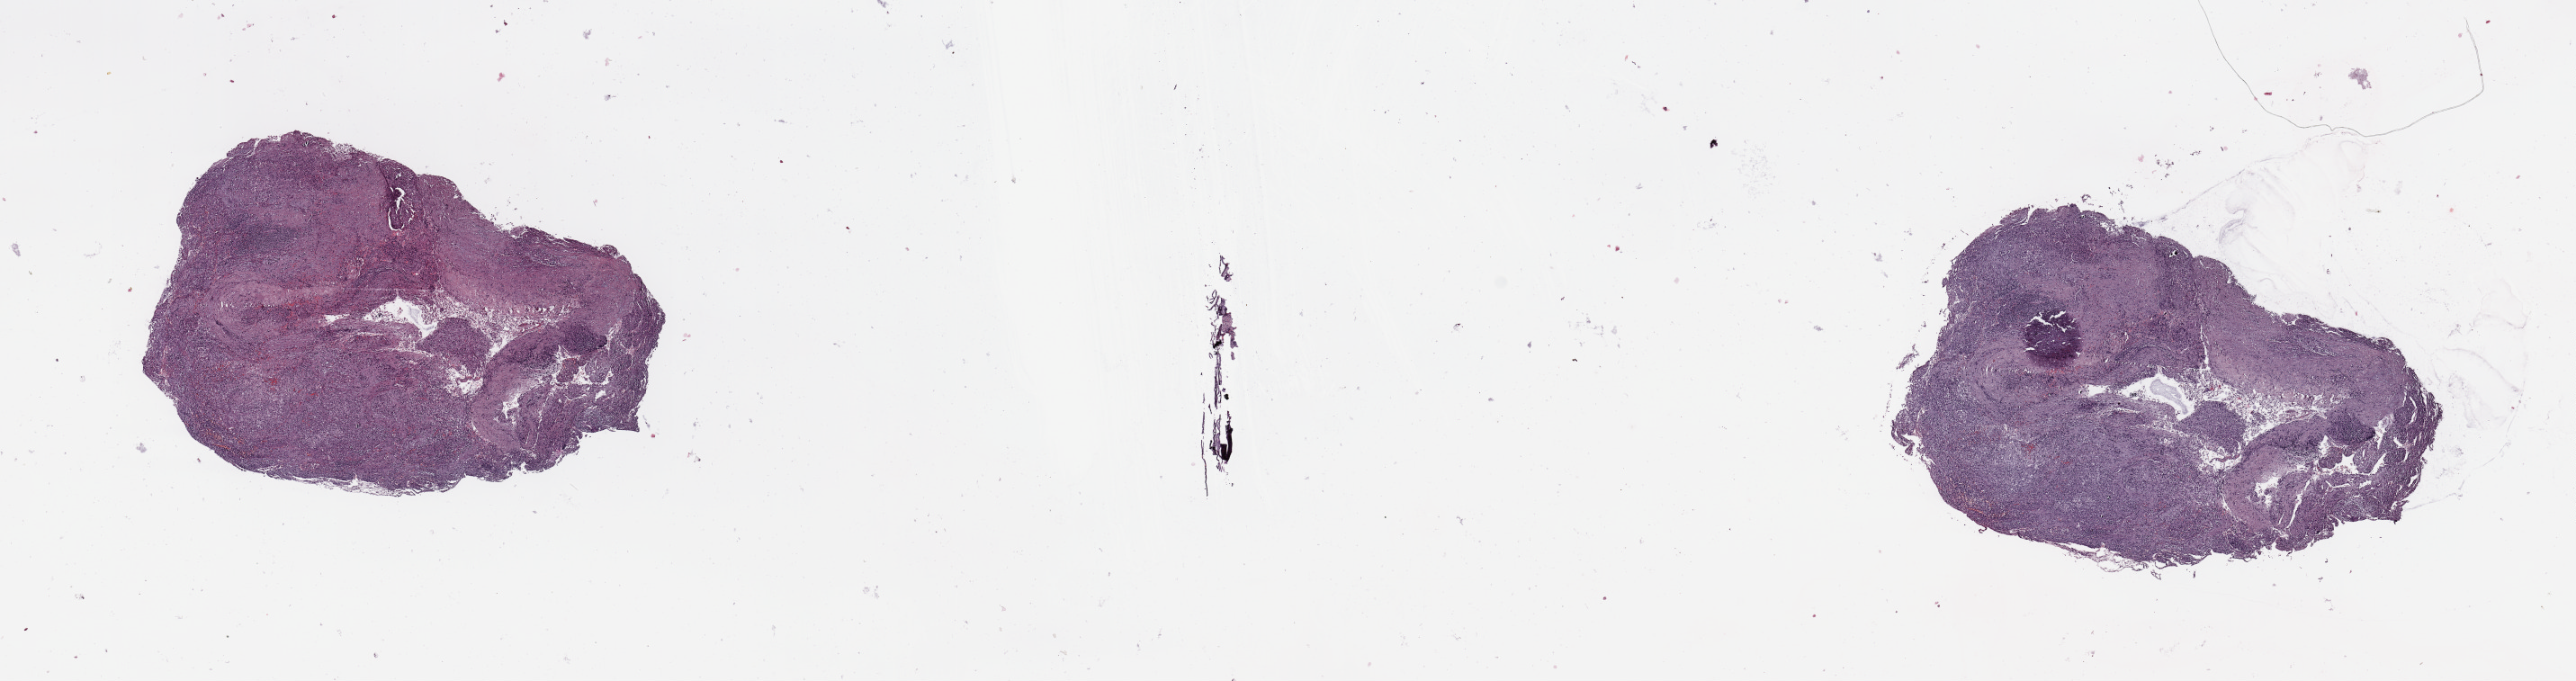
H&E whole-slide image, a low-resolution overview of the entire scanned area, about 22.6 x 6.0 mm (slide scanned at 20x). Tumour tissue sample, sampled site: lung. Male, 55 y/o. Histologic grade: G3 (poorly differentiated). Composition of this section per pathologist review: tumour nuclei 75%, necrosis 5%.
Diagnosis: Adenocarcinoma, NOS. AJCC pathologic stage: IV. Primary tumour site (as recorded): right upper lobe.